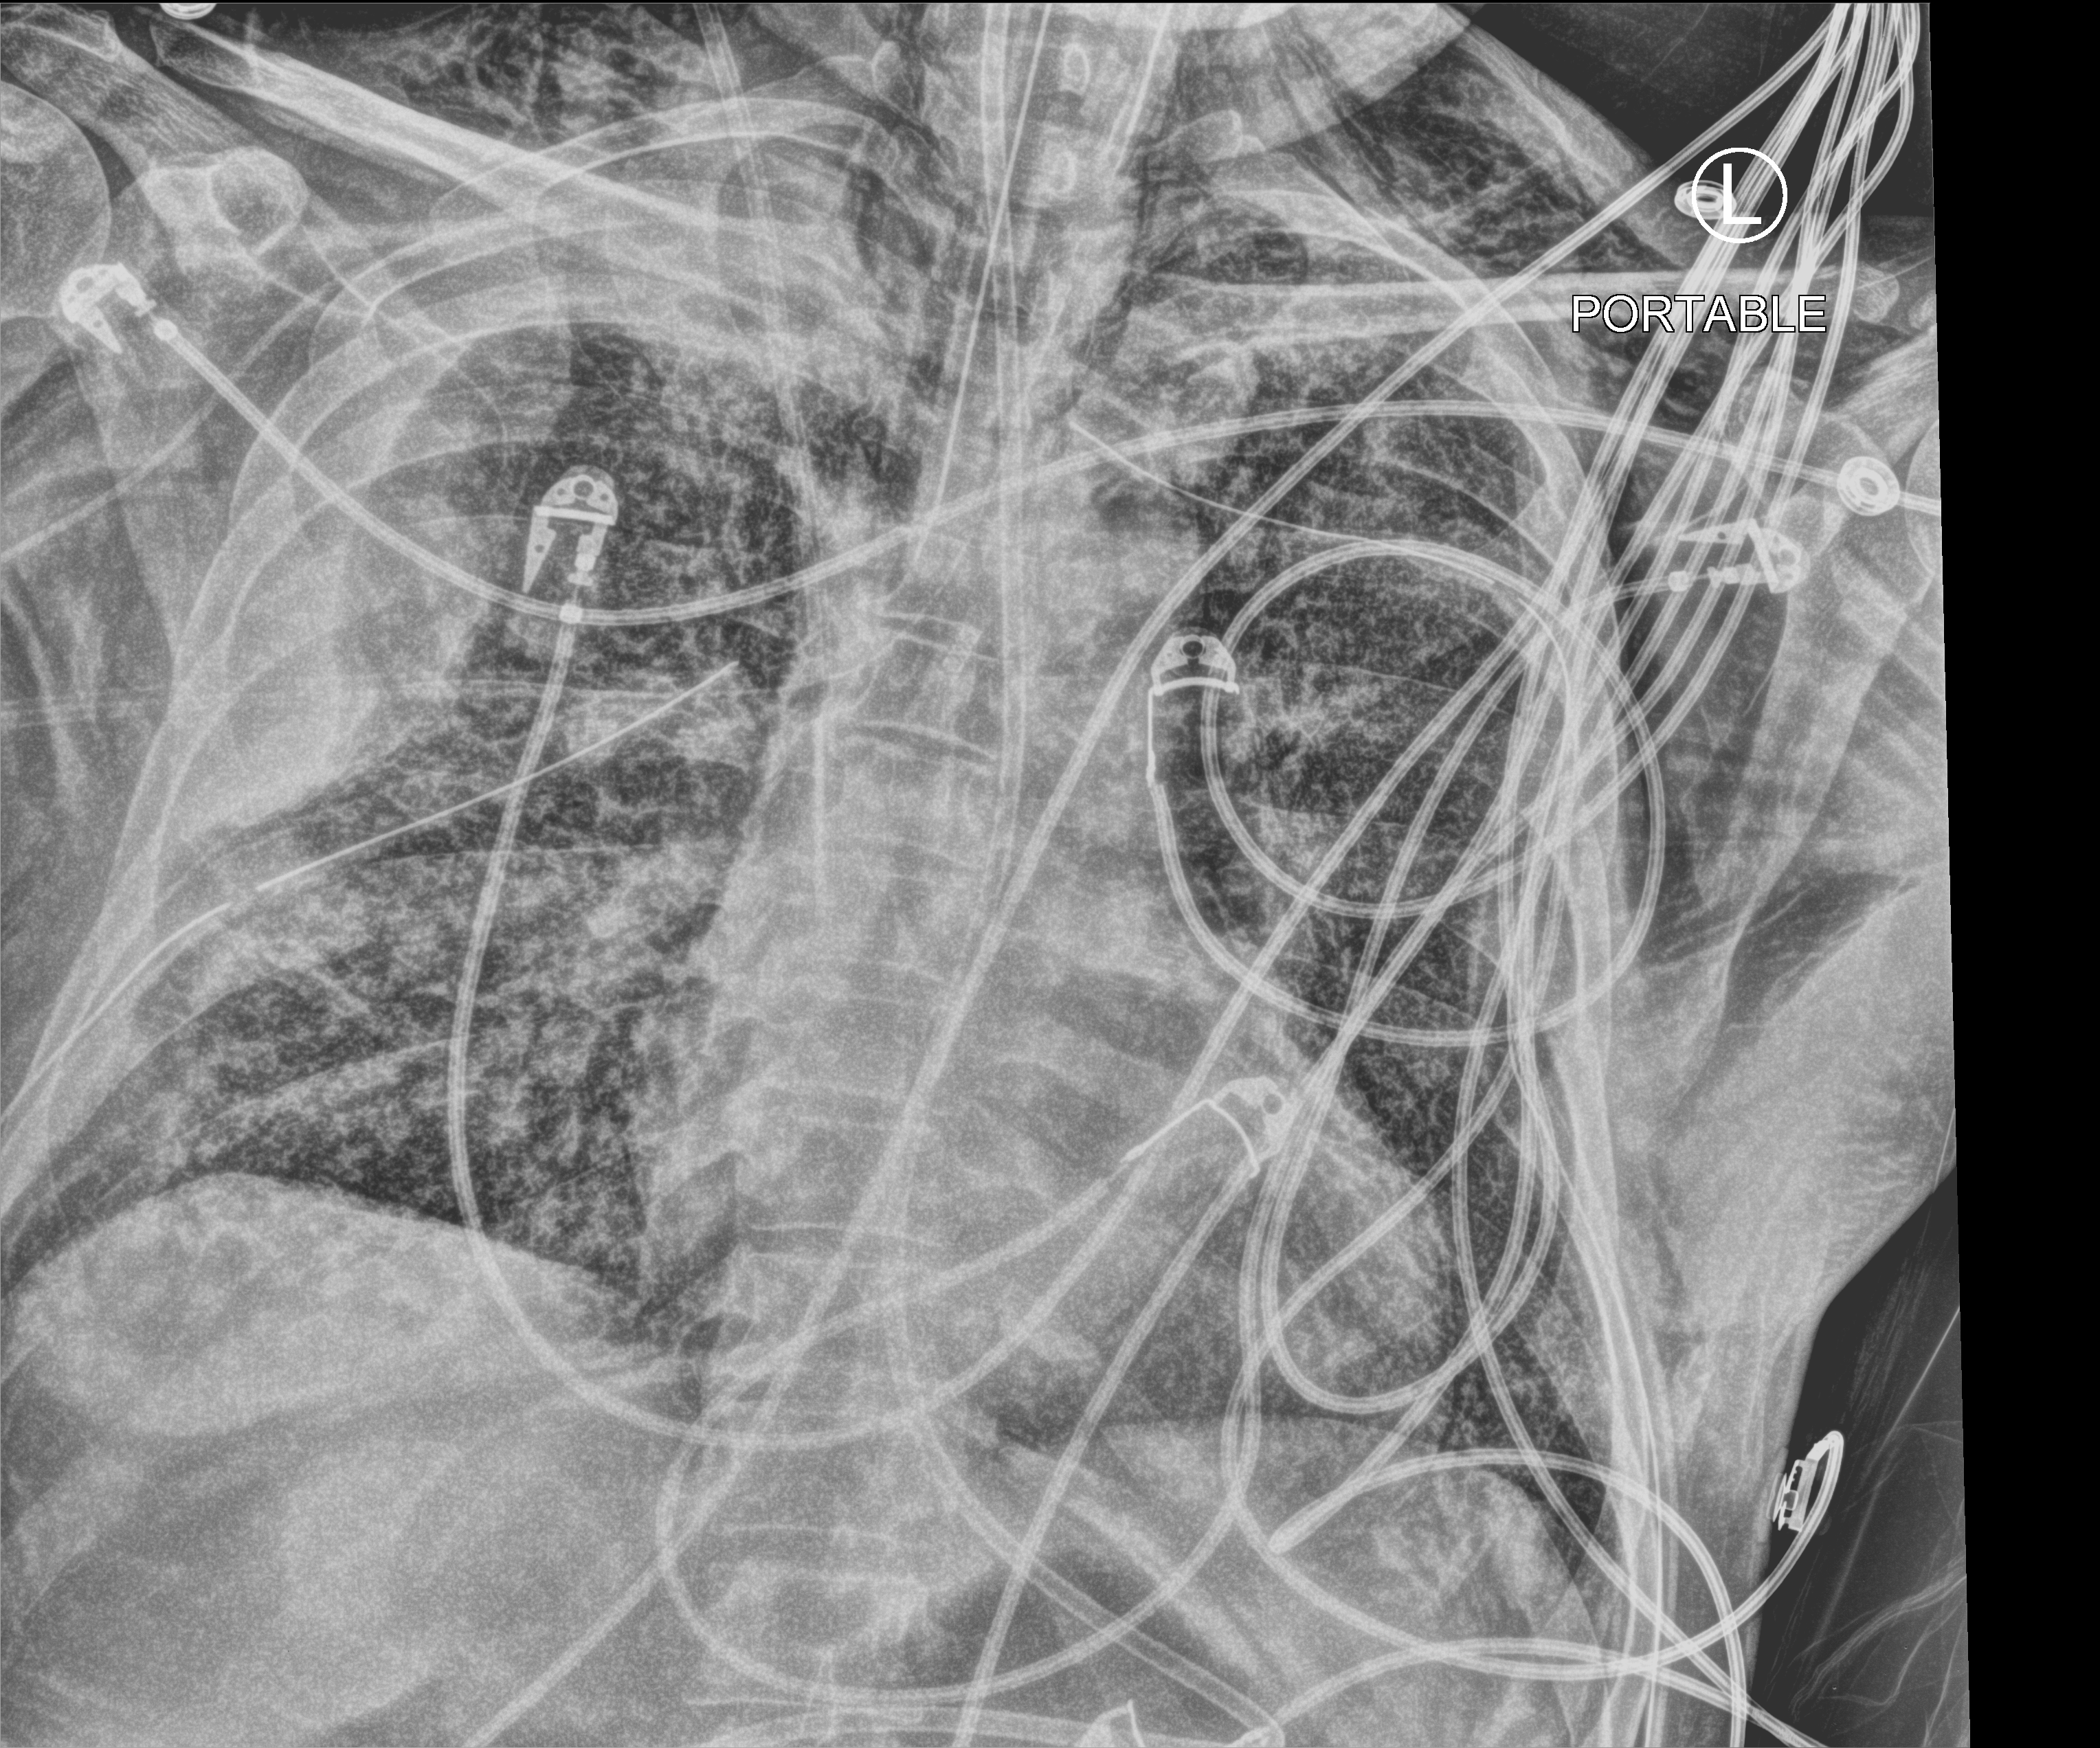
Chest X-ray (portable), anteroposterior (AP) projection. Patient hospitalised with COVID-19; male, aged 18–59 years.
From the hospital-stay record, not from the radiograph (when in the stay this image was taken is not recorded): admitted to intensive care during this hospital stay: yes; mechanically ventilated during this hospital stay: yes.